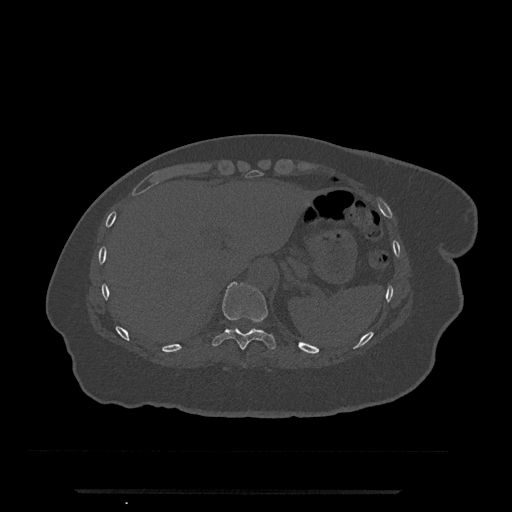
CT including the spine, one axial slice. Slice 282 of 797 in the series (ordered by position). Reconstruction kernel Br40s/3. Bone window (W 1800 / L 400 HU). 512 × 512 image matrix, field of view 440 × 440 mm. Patient: female, 51 years. Case-level facts recorded for this patient, not image findings: primary cancer: neuro.
Outlined on this slice (semi-automatically segmented with operator editing):
- T10 vertebra: bounding box (x1, y1, x2, y2) in pixels: (212, 282, 276, 350)